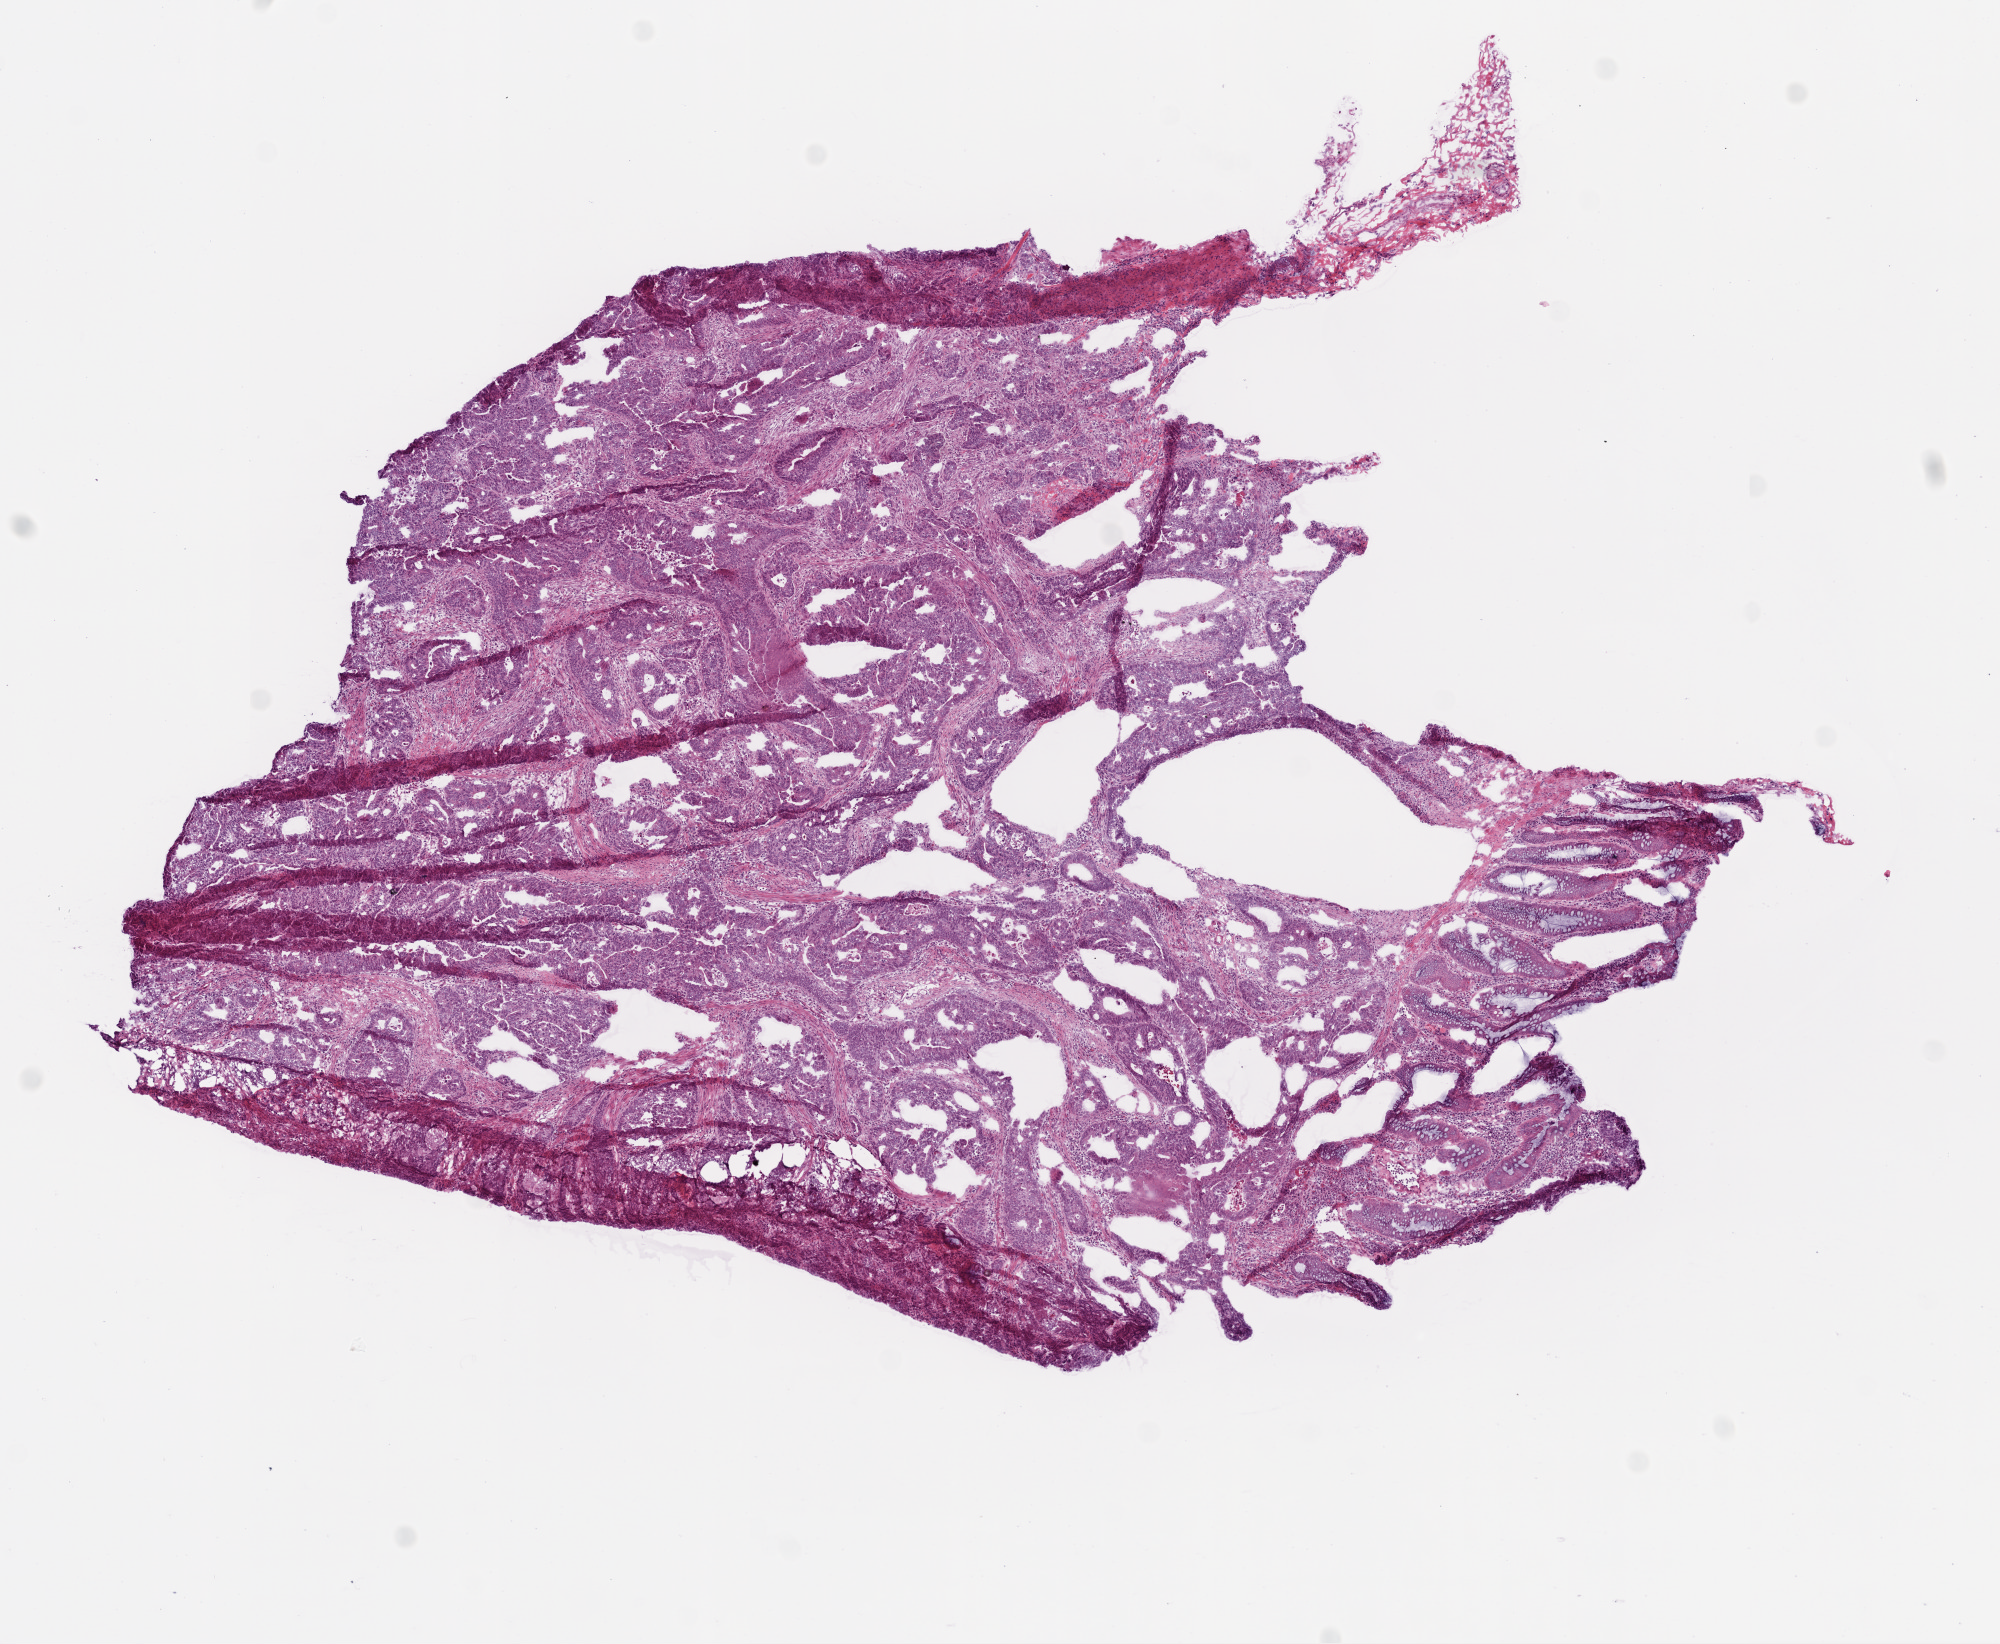
Digitized H&E tissue section (whole slide), whole scanned area (about 8.0 x 6.6 mm) shown as a low-resolution overview. Frozen section from the top of the tissue portion. Primary tumour sample from the colon. Male, age 67 years at initial diagnosis. Composition of this section per pathologist review: tumour cells 85%, tumour nuclei 85%, normal cells 0%, stromal cells 10%, necrosis 5%.
Histologic diagnosis: Adenocarcinoma, NOS. AJCC pathologic stage: I (6th edition).